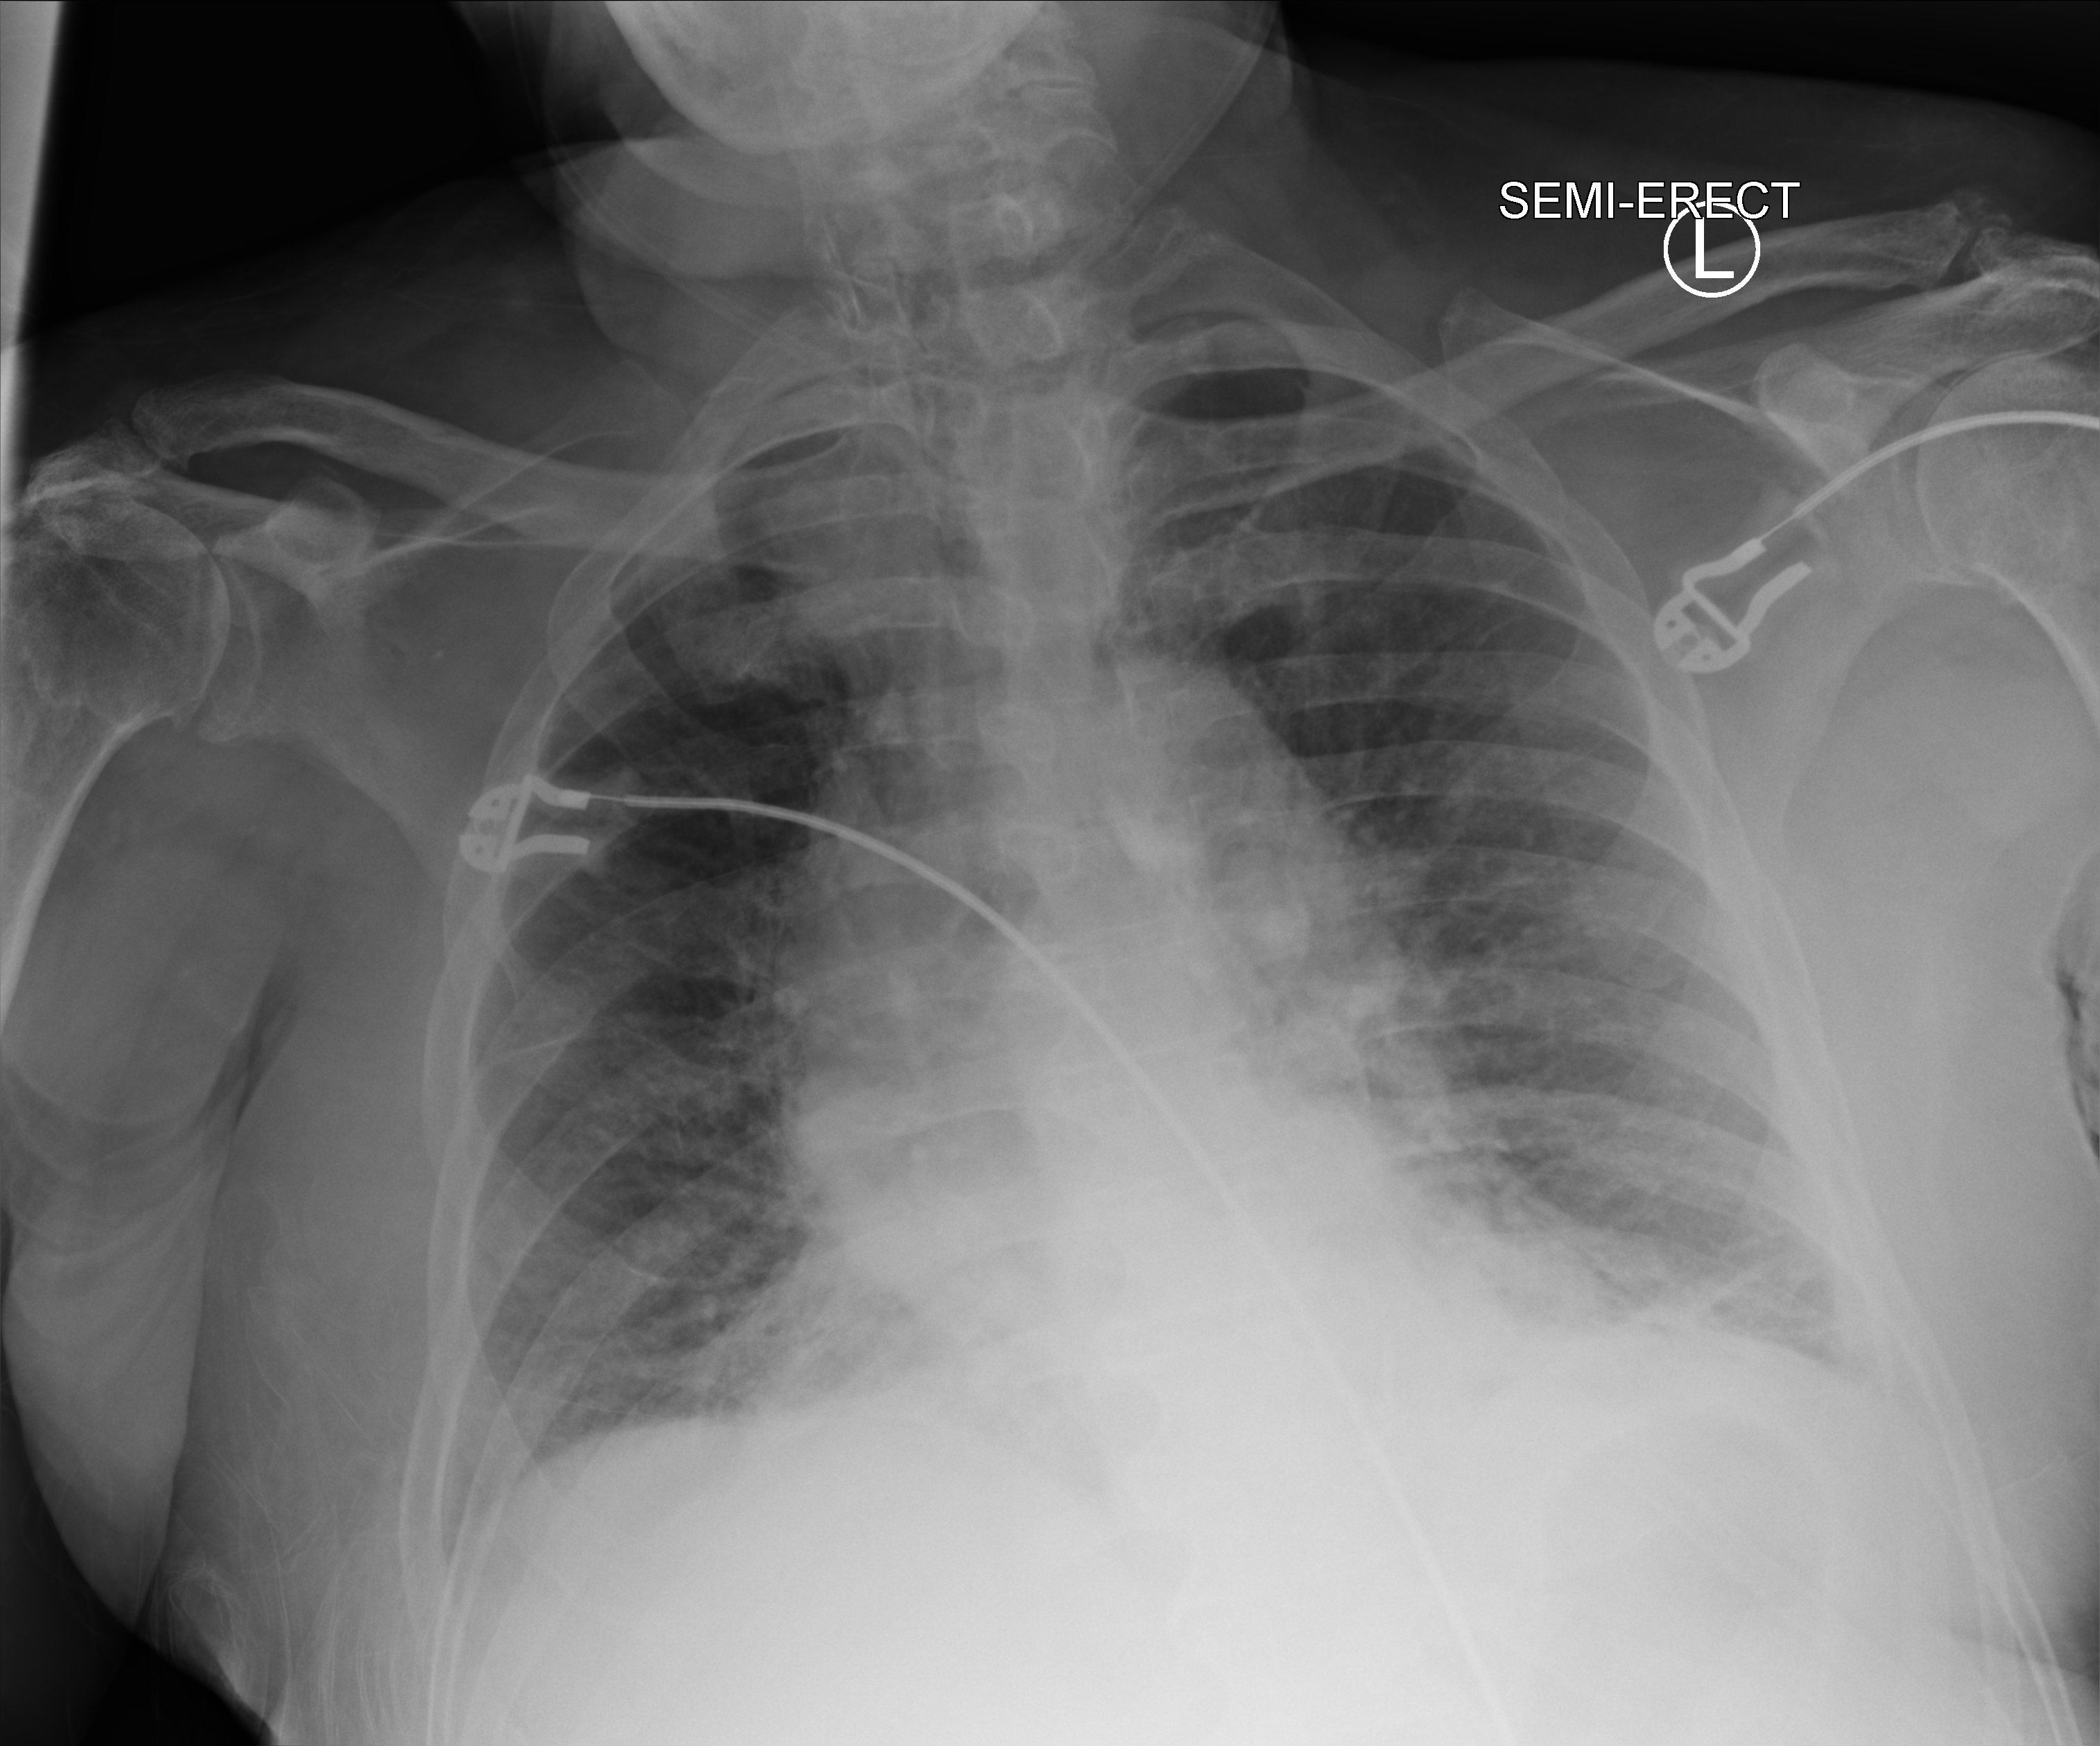
Portable chest radiograph, anteroposterior (AP) projection. Patient hospitalised with COVID-19; male, aged 75–90 years.
From the hospital-stay record, not from the radiograph (when in the stay this image was taken is not recorded):
- admitted to intensive care during this hospital stay: no
- mechanically ventilated during this hospital stay: no